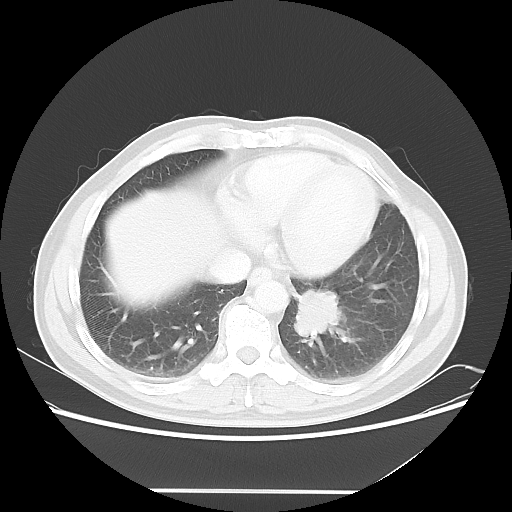
Chest CT, one axial slice; position 16 of 53 along the scan axis; reconstruction kernel LUNG; lung window (W 1500 / L -600 HU); 5 mm slice thickness; 512 × 512 image matrix, field of view 385 × 385 mm. Male patient, age 61 years. Case-level facts recorded for this patient, not image findings: clinical TNM (as recorded): T1c N0 M0.
Annotated regions visible in this slice (bounding box drawn by a radiologist):
- lung tumour (recorded histology: adenocarcinoma): bounding box (x1, y1, x2, y2) in pixels: (288, 283, 347, 348)